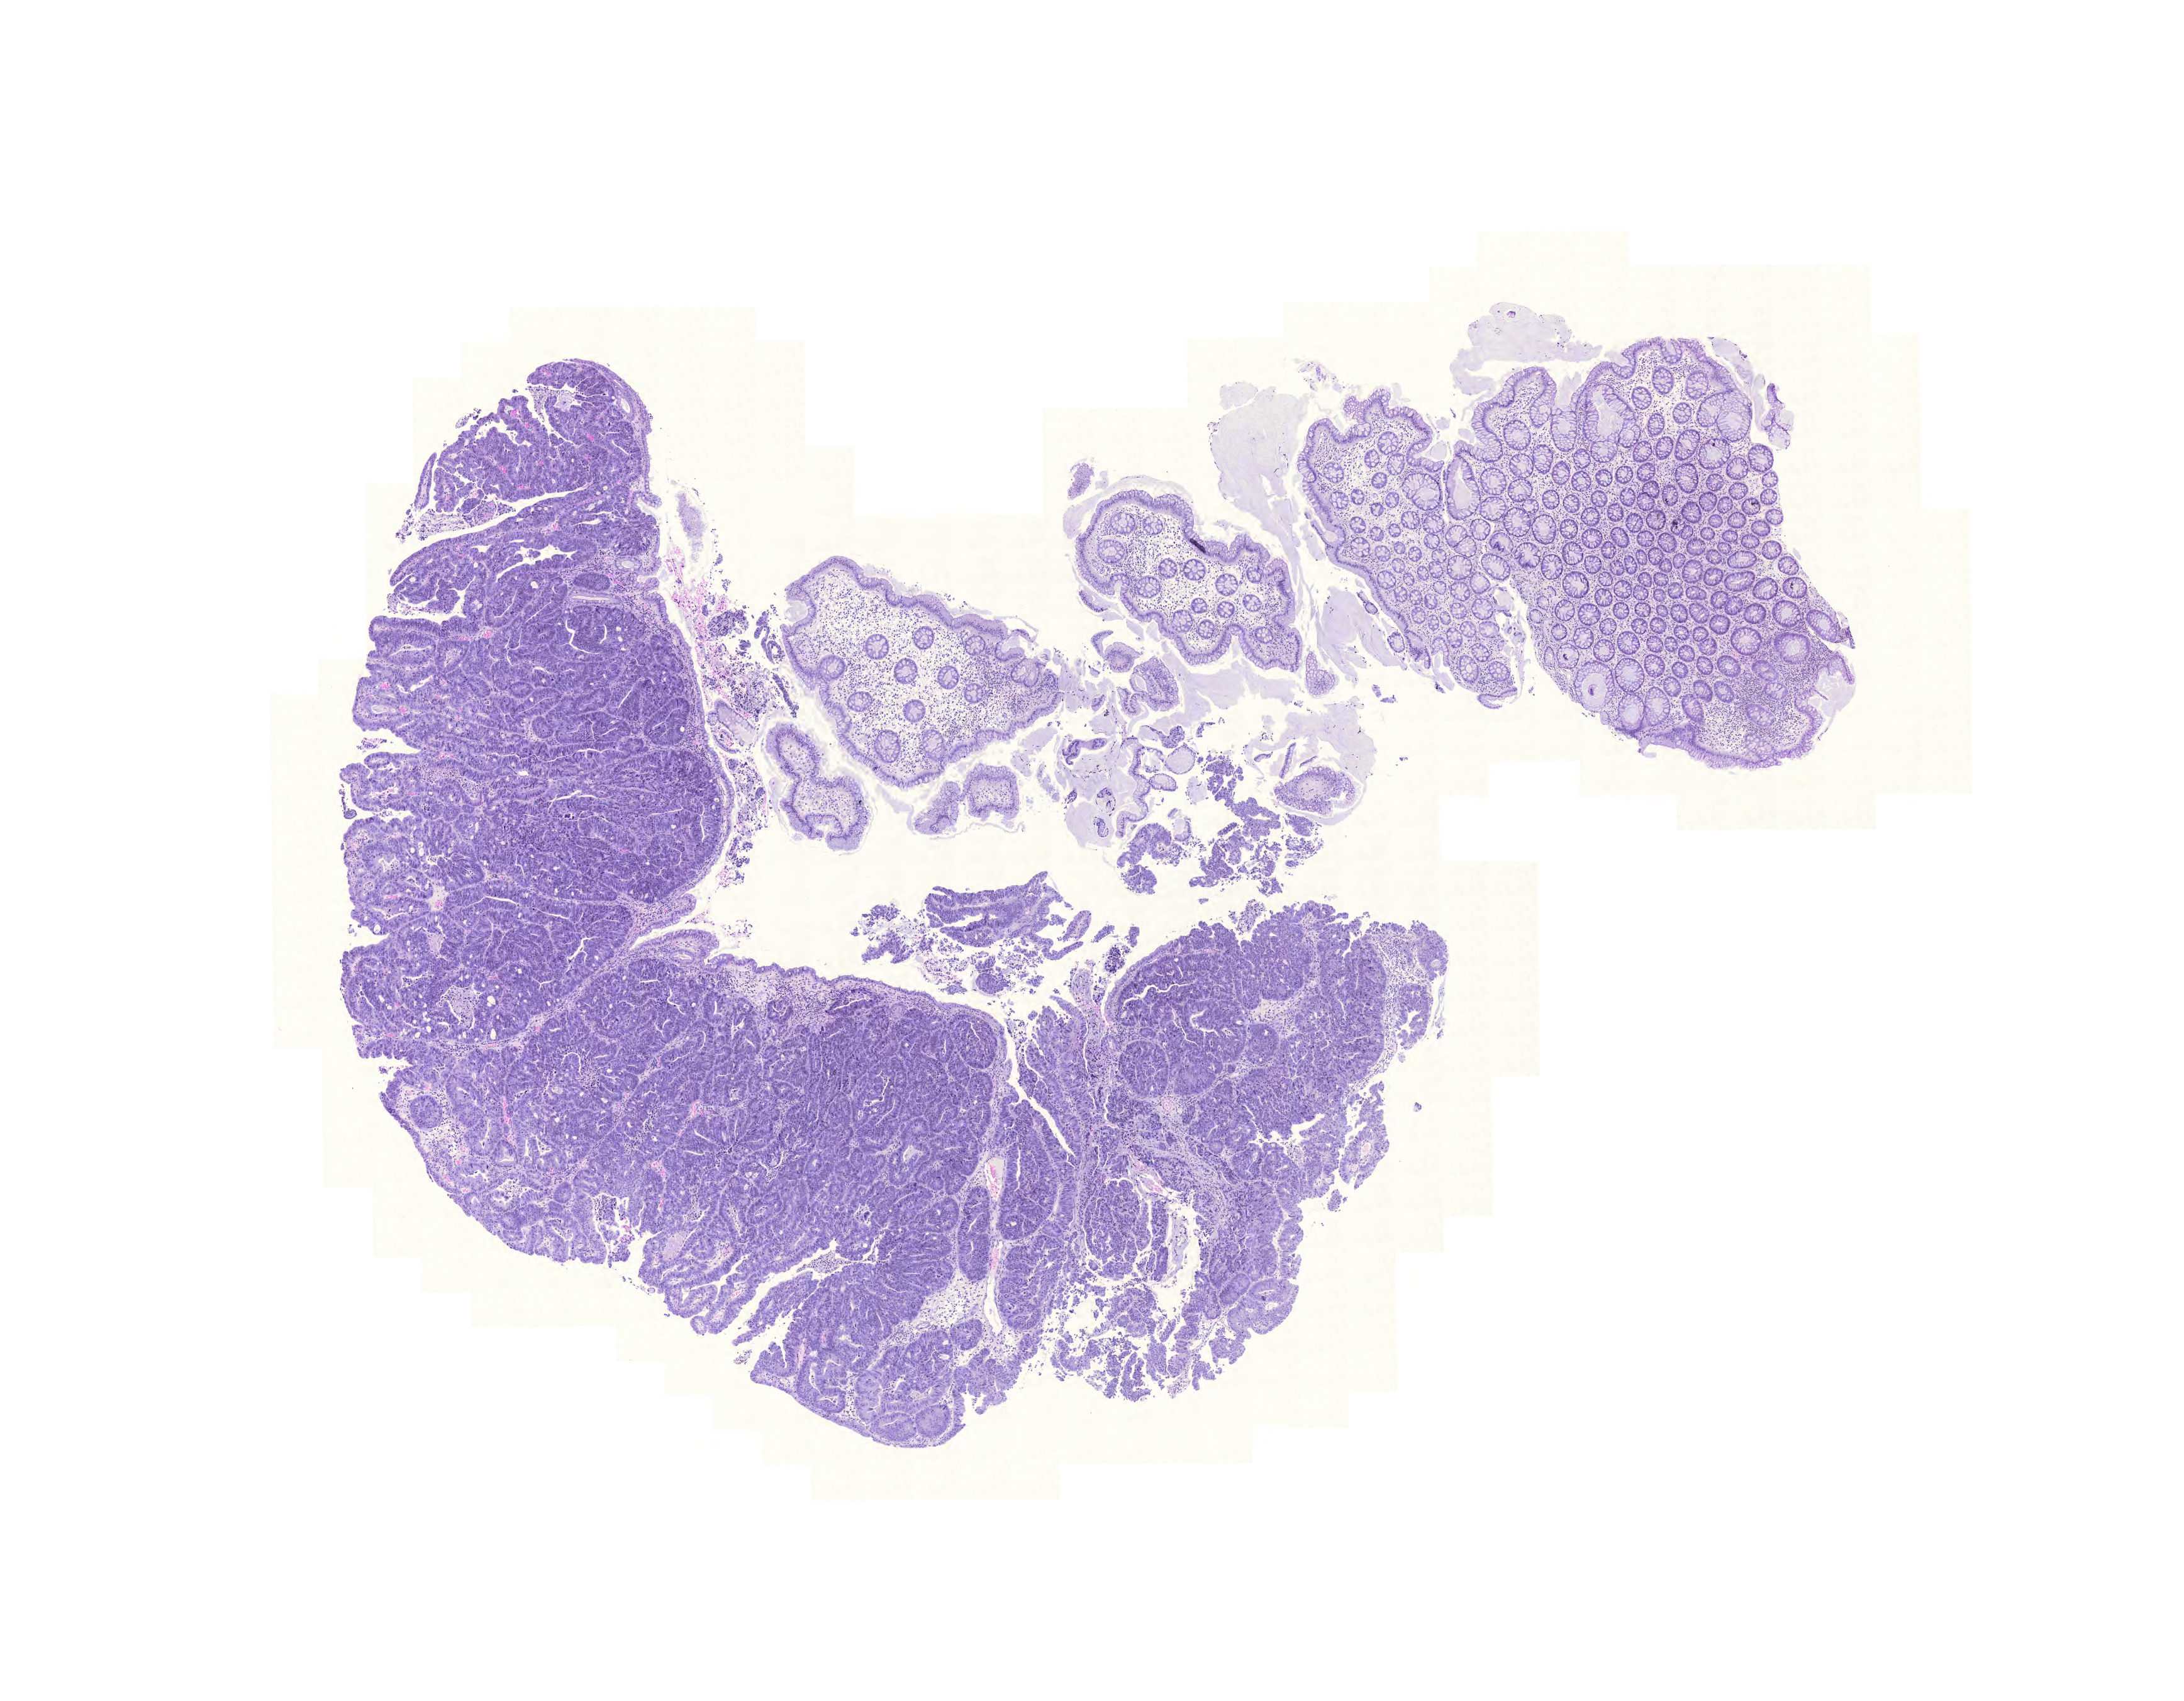
Hematoxylin and eosin (H&E) stained whole-slide image, low-resolution overview of the scanned area, about 12.9 x 10.1 mm (acquisition: 20x scan); formalin-fixed paraffin-embedded (FFPE) diagnostic section; primary tumour sample from the rectum. Female patient; age at initial diagnosis 85 years.
Pathologic diagnosis: Adenocarcinoma, NOS (colon, NOS).